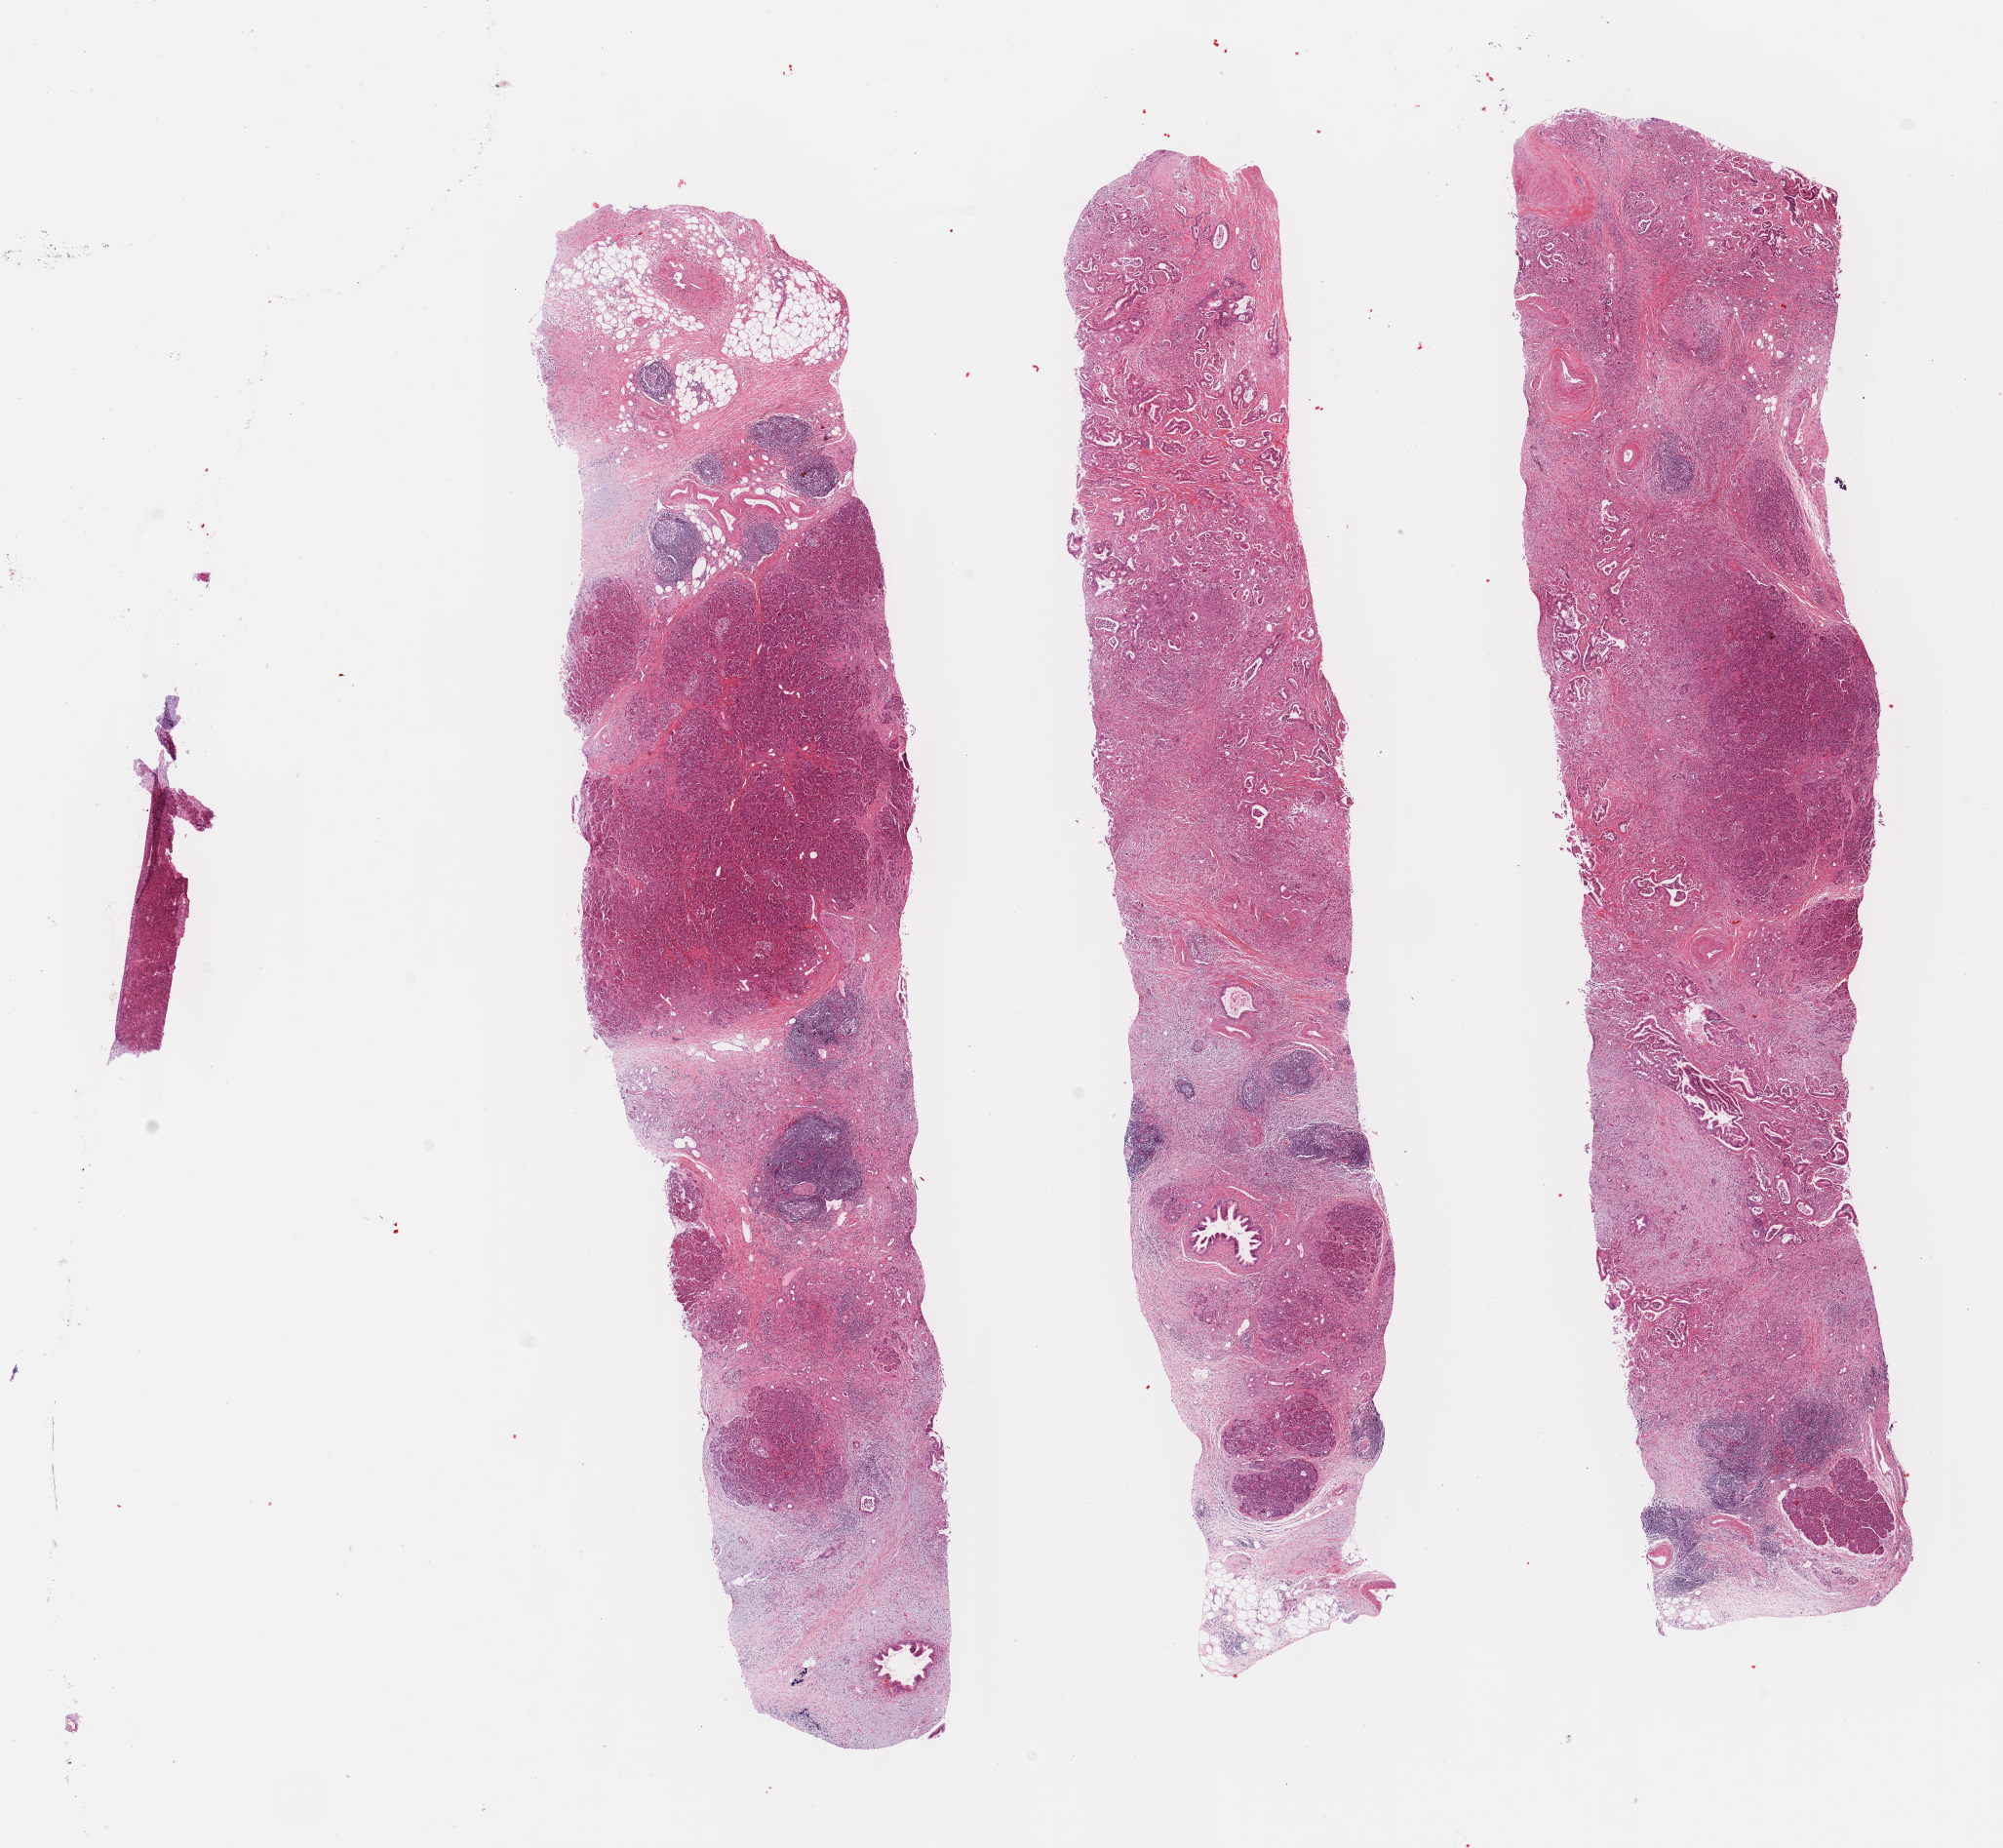
H&E whole-slide image, shown as a low-resolution overview of the whole scanned area (about 16.6 x 15.3 mm); formalin-fixed paraffin-embedded (FFPE) diagnostic section; primary tumour sample from the pancreas. Male, age 70 years at initial diagnosis. Histologic grade: G2 (moderately differentiated).
AJCC pathologic stage: IIA (7th edition). Pathologic diagnosis: Infiltrating duct carcinoma, NOS.